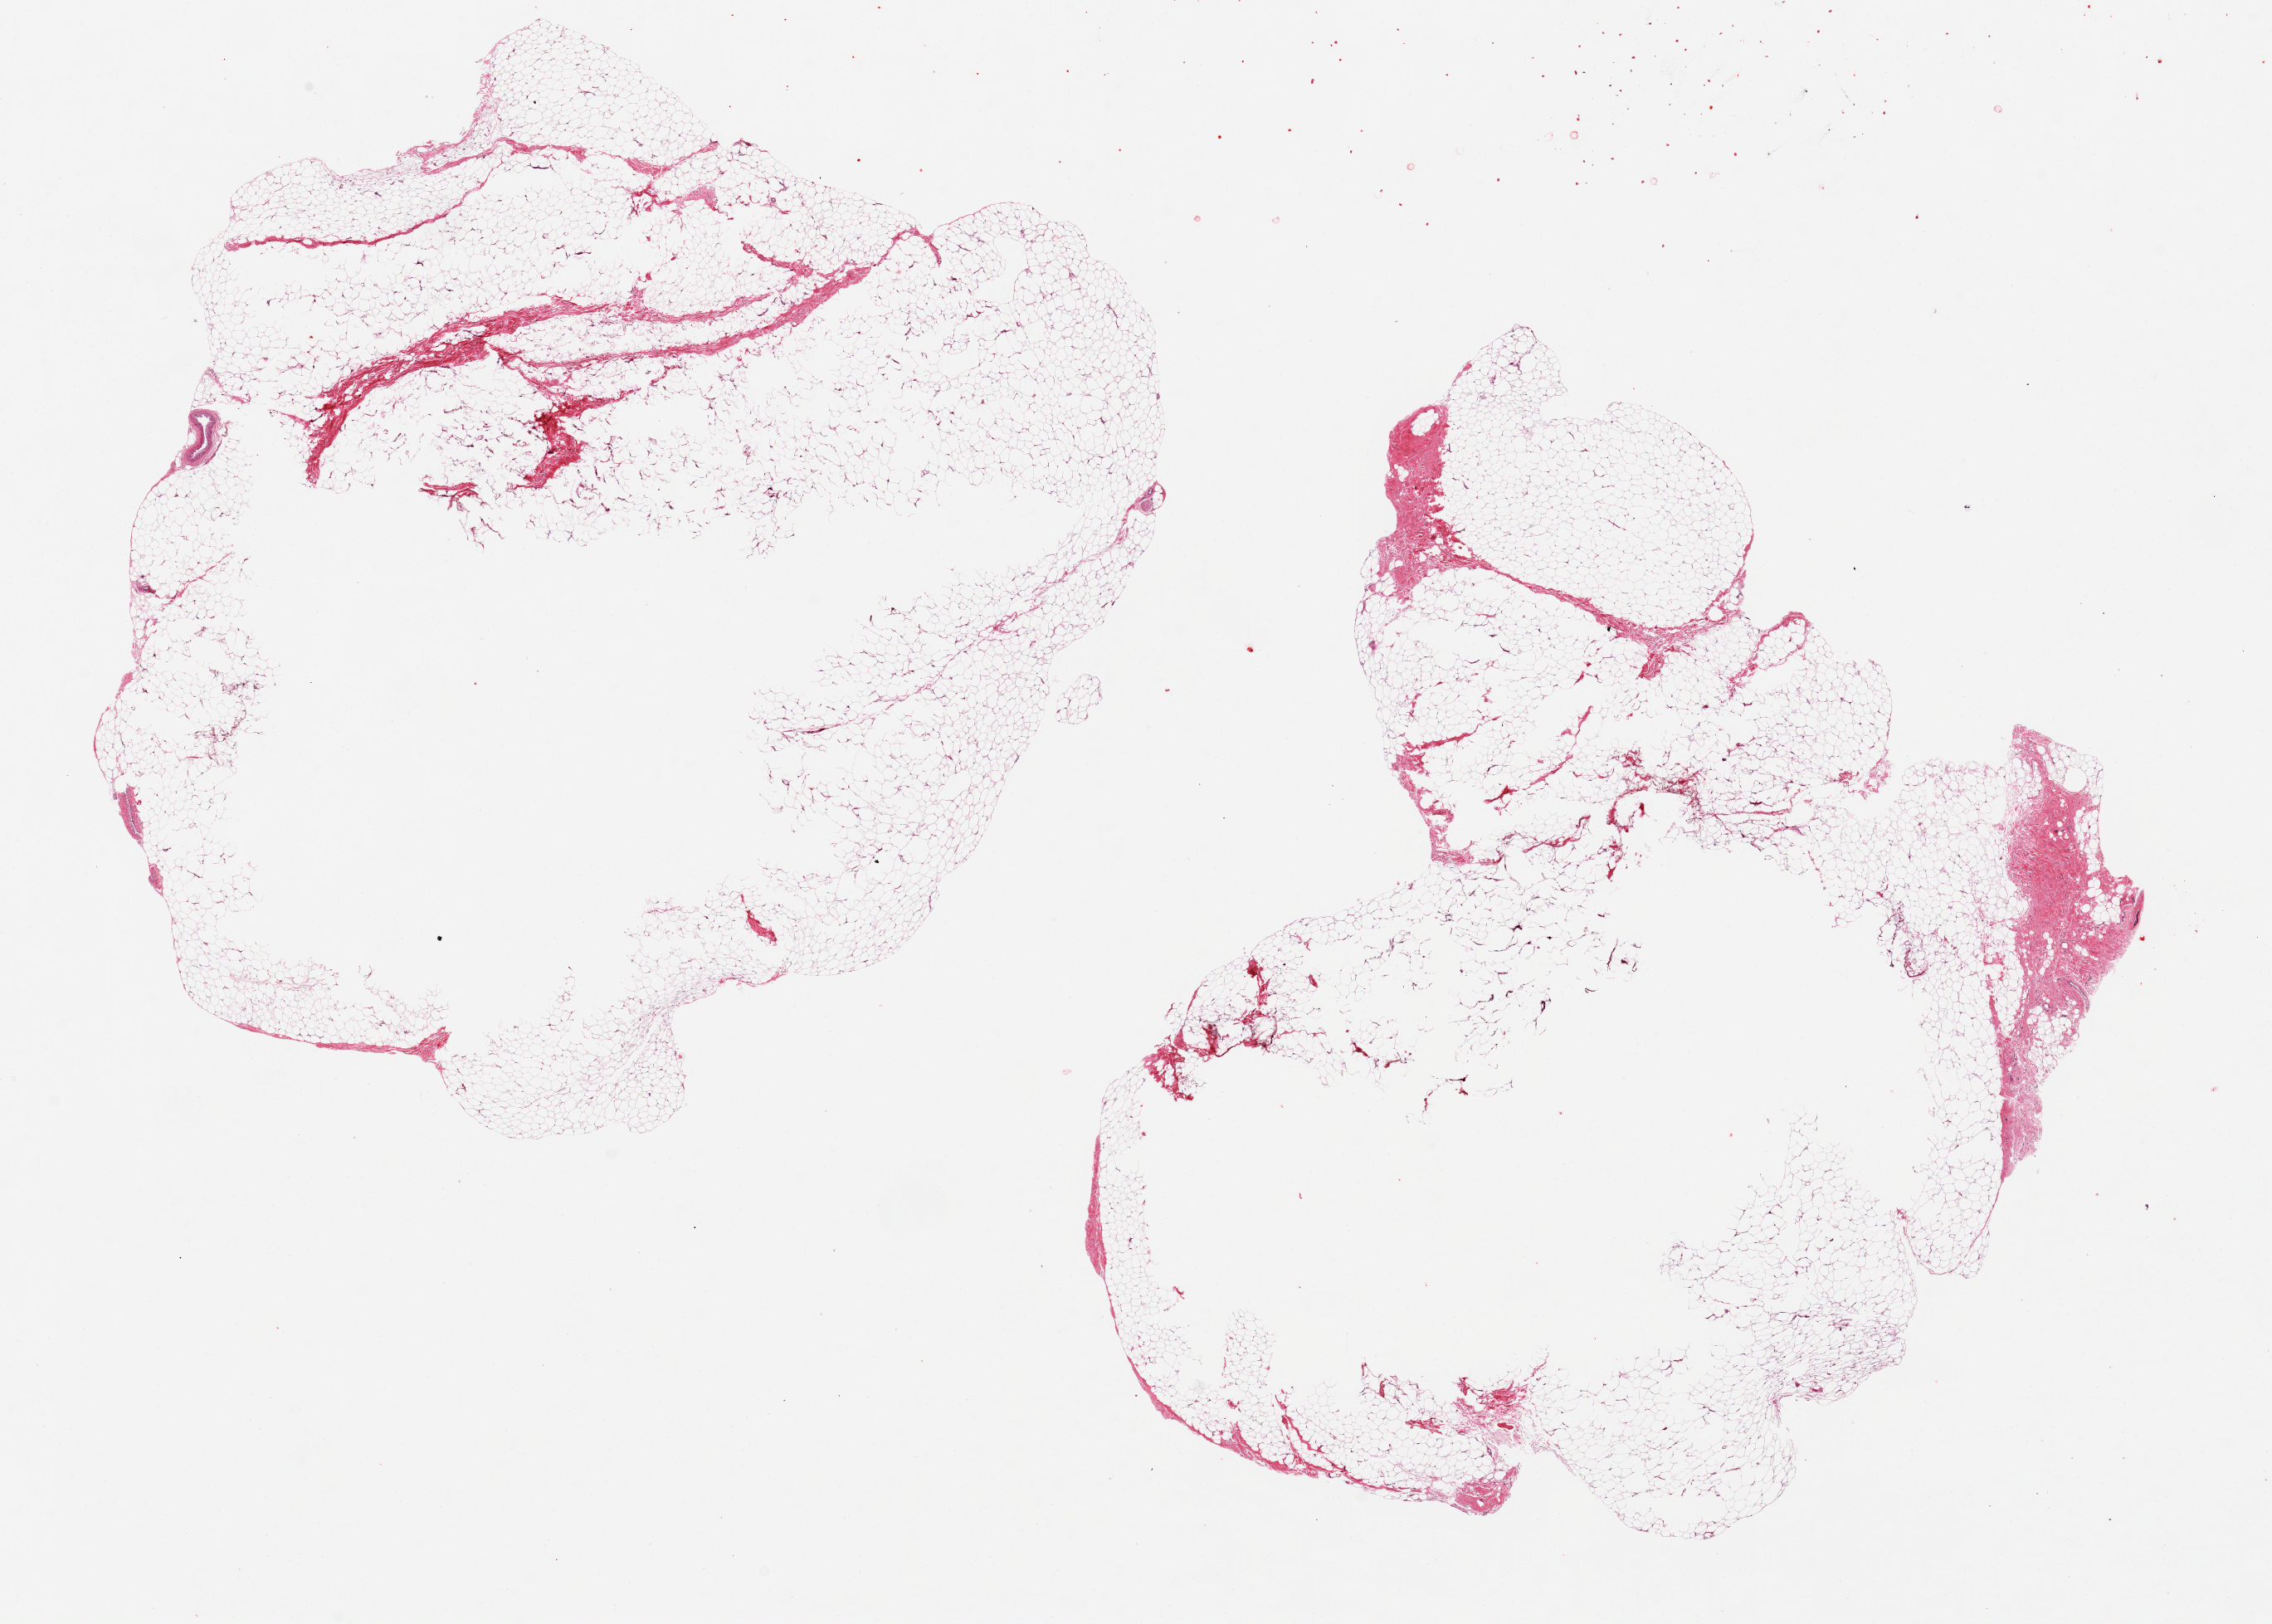
Haematoxylin and eosin whole-slide image, brightfield, whole scanned area (about 21.7 x 15.5 mm) shown as a low-resolution overview, PAXgene-fixed, paraffin-embedded tissue, target tissue: breast, donor tissue sample. Male donor.
Pathologist's review note for this sample: 2 ~8.5x8mm aliquots; no visible ductal elements. Extreme separation of sections.